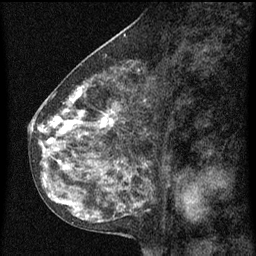
Breast MRI (dynamic contrast-enhanced), one sagittal slice. Dynamic contrast-enhanced series, image 2 of 3 at this slice position (ordered by acquisition). 1.5 T. TE 4.2 ms, TR 8 ms. 2 mm slice thickness. 256 × 256 image matrix, field of view 180 × 180 mm. Patient: female, 55 years.
Annotated regions visible in this slice (semi-automatically segmented with operator editing):
- analysis volume of interest (the breast-tissue region the enhancement analysis was run in; not a lesion): bounding box <34,68,159,151> (left, top, right, bottom; pixels)
- tumour enhancement mask (voxels above the 70 % enhancement threshold inside the analysis volume of interest): <38,84,119,151>